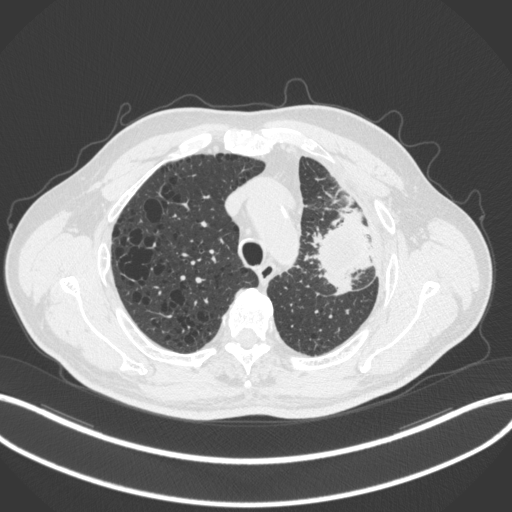
Chest CT, one axial slice. Position 235 of 286 along the scan axis. Reconstruction kernel B31f. 120 kVp. Lung window (W 1500 / L -600 HU). 1 mm slice thickness. 512 × 512 image matrix, field of view 400 × 400 mm. Male patient, age 68 years. From the clinical record (not read from this slice): clinical TNM (as recorded): T3 N3 M1.
Structures marked on this image (bounding box drawn by a radiologist):
- lung tumour (recorded histology: adenocarcinoma): box from (x=312, y=206) to (x=381, y=296) px